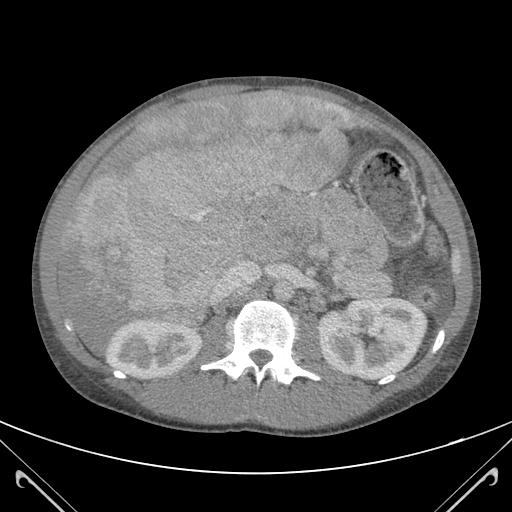
Contrast-enhanced abdominal CT (liver protocol), one axial slice. Position 64 of 118 along the scan axis. Soft-tissue window (W 400 / L 40 HU). 512 × 512 image matrix. Case-level facts recorded for this patient, not image findings: diagnosis: hepatocellular carcinoma (patient treated with transarterial chemoembolisation; whether this scan precedes or follows treatment is not stated here); TNM stage (as recorded): Stage-IIIB; Child-Pugh class: A; tumour nodularity: uninodular.
Structures marked on this image (semi-automatic segmentation, software-assisted and operator-edited):
- abdominal aorta: bounding box (x1, y1, x2, y2) in pixels: (273, 279, 293, 302)
- liver parenchyma outside the tumour (the mass and vessels are separate outlines, so this box may not span the whole liver): (57, 91, 357, 352)
- mass: (64, 93, 346, 328)
- liver vessels: (132, 100, 350, 308)